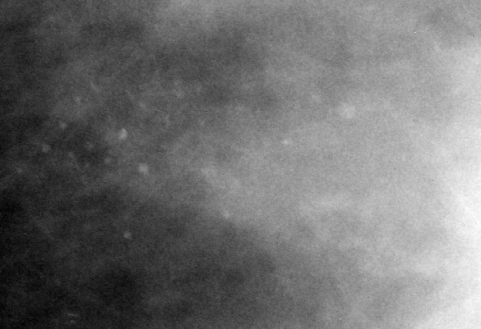
Region of interest cut from a scanned film mammogram (one marked finding); left breast; CC view; BI-RADS breast density category 3 (scale 1–4).
Marked abnormality: calcifications, morphology pleomorphic, distribution segmental; BI-RADS assessment category 4; subtlety rating 3 on a 1 (subtle) to 5 (obvious) scale; pathology (as recorded): benign.